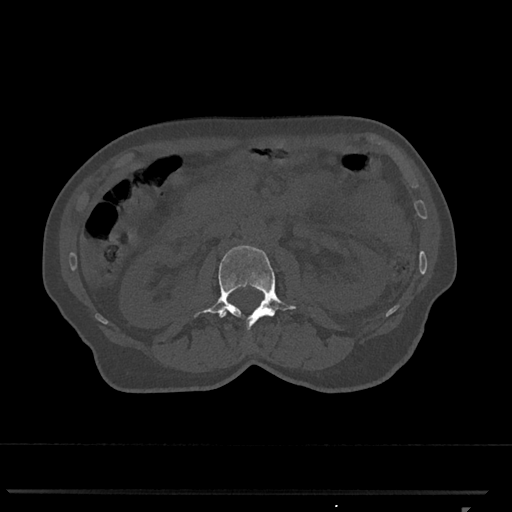
CT including the spine, one axial slice. Slice 341 of 793 in the series (ordered by position). Reconstruction kernel Br40s/3. Bone window (W 1800 / L 400 HU). 0.5 mm slice thickness. 512 × 512 image matrix, field of view 380 × 380 mm. Female patient, age 62 years. Case-level facts recorded for this patient, not image findings: primary cancer: renal.
Outlined on this slice (semi-automatic segmentation, software-assisted and operator-edited):
- L2 vertebra: bounding box <194,245,296,330> (left, top, right, bottom; pixels)